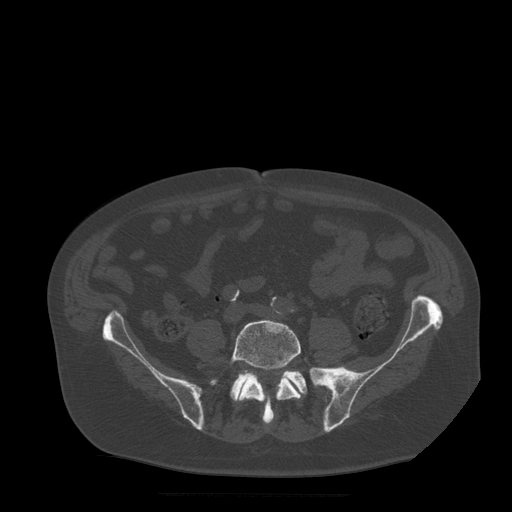
CT including the spine, one axial slice; slice 84 of 522 in the series (ordered by position); bone window (W 1800 / L 400 HU); 1.25 mm slice thickness; 512 × 512 image matrix, field of view 420 × 420 mm. Patient age 72 years. From the clinical record (not read from this slice): primary cancer: prostate.
Structures marked on this image (semi-automatic segmentation, software-assisted and operator-edited):
- L5 vertebra: box from (x=230, y=320) to (x=306, y=424) px